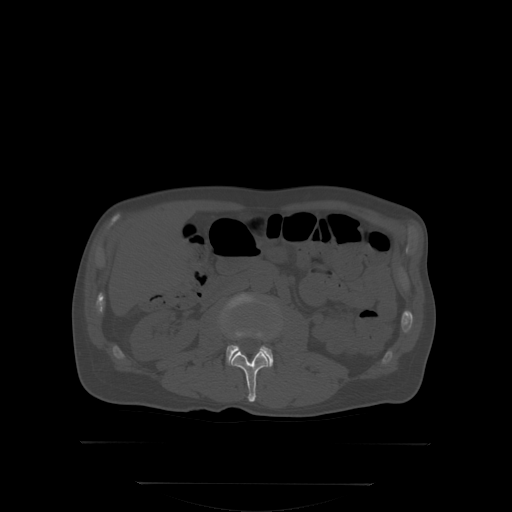
CT including the spine, one axial slice. Bone window (W 1800 / L 400 HU). 2.5 mm slice thickness. 512 × 512 image matrix. Male patient, age 58 years. Case-level facts recorded for this patient, not image findings: primary cancer: prostate.
Outlined on this slice (semi-automatically segmented with operator editing):
- L2 vertebra: bounding box <232,334,269,402> (left, top, right, bottom; pixels)
- L3 vertebra: <223,295,279,367>